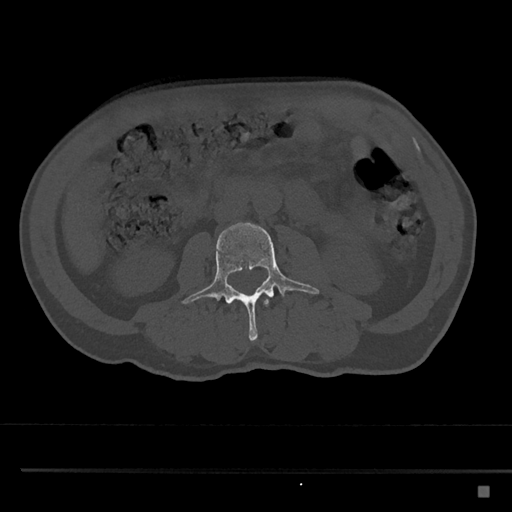
CT including the spine, one axial slice. Reconstruction kernel Br40s/3. 120 kVp. Bone window (W 1800 / L 400 HU). 0.5 mm slice thickness. 512 × 512 image matrix, field of view 391 × 391 mm. Patient: male, 59 years. From the clinical record (not read from this slice): primary cancer: prostate.
Annotated regions visible in this slice (semi-automatically segmented with operator editing):
- L2 vertebra: bounding box <228,299,269,306> (left, top, right, bottom; pixels)
- L3 vertebra: <182,222,320,343>